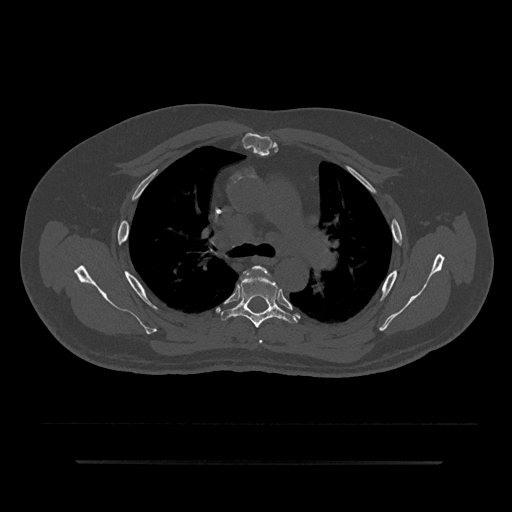
CT including the spine, one axial slice; position 580 of 797 along the scan axis; 120 kVp; bone window (W 1800 / L 400 HU); 512 × 512 image matrix, field of view 464 × 464 mm. Patient: male, 59 years. From the clinical record (not read from this slice): primary cancer: bile ducts.
Annotated regions visible in this slice (semi-automatic segmentation, software-assisted and operator-edited):
- T4 vertebra: bounding box [x1, y1, x2, y2] px = [252, 265, 268, 343]
- T5 vertebra: [221, 272, 298, 328]